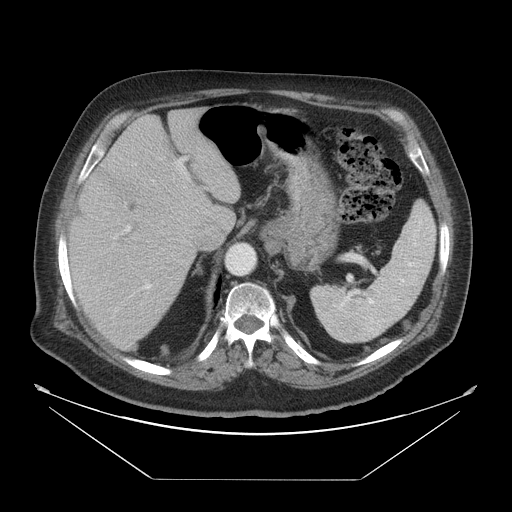
Contrast-enhanced abdominal CT, one axial slice. Position 36 of 45 along the scan axis. 120 kVp. Soft-tissue window (W 400 / L 40 HU). 512 × 512 image matrix, field of view 463 × 463 mm. Male patient, age 87 years. Case-level facts recorded for this patient, not image findings: diagnosis: colorectal cancer liver metastases, imaged before liver resection; multiple liver metastases: no.
Annotated regions visible in this slice (manually delineated by an expert):
- liver: bounding box [x1, y1, x2, y2] px = [68, 108, 242, 351]
- planned liver remnant (the part of the liver to remain after resection): [112, 108, 242, 203]
- portal vein (with intrahepatic branches): [122, 156, 190, 290]
- liver metastasis: [126, 219, 145, 241]
- liver metastasis: [94, 163, 145, 211]